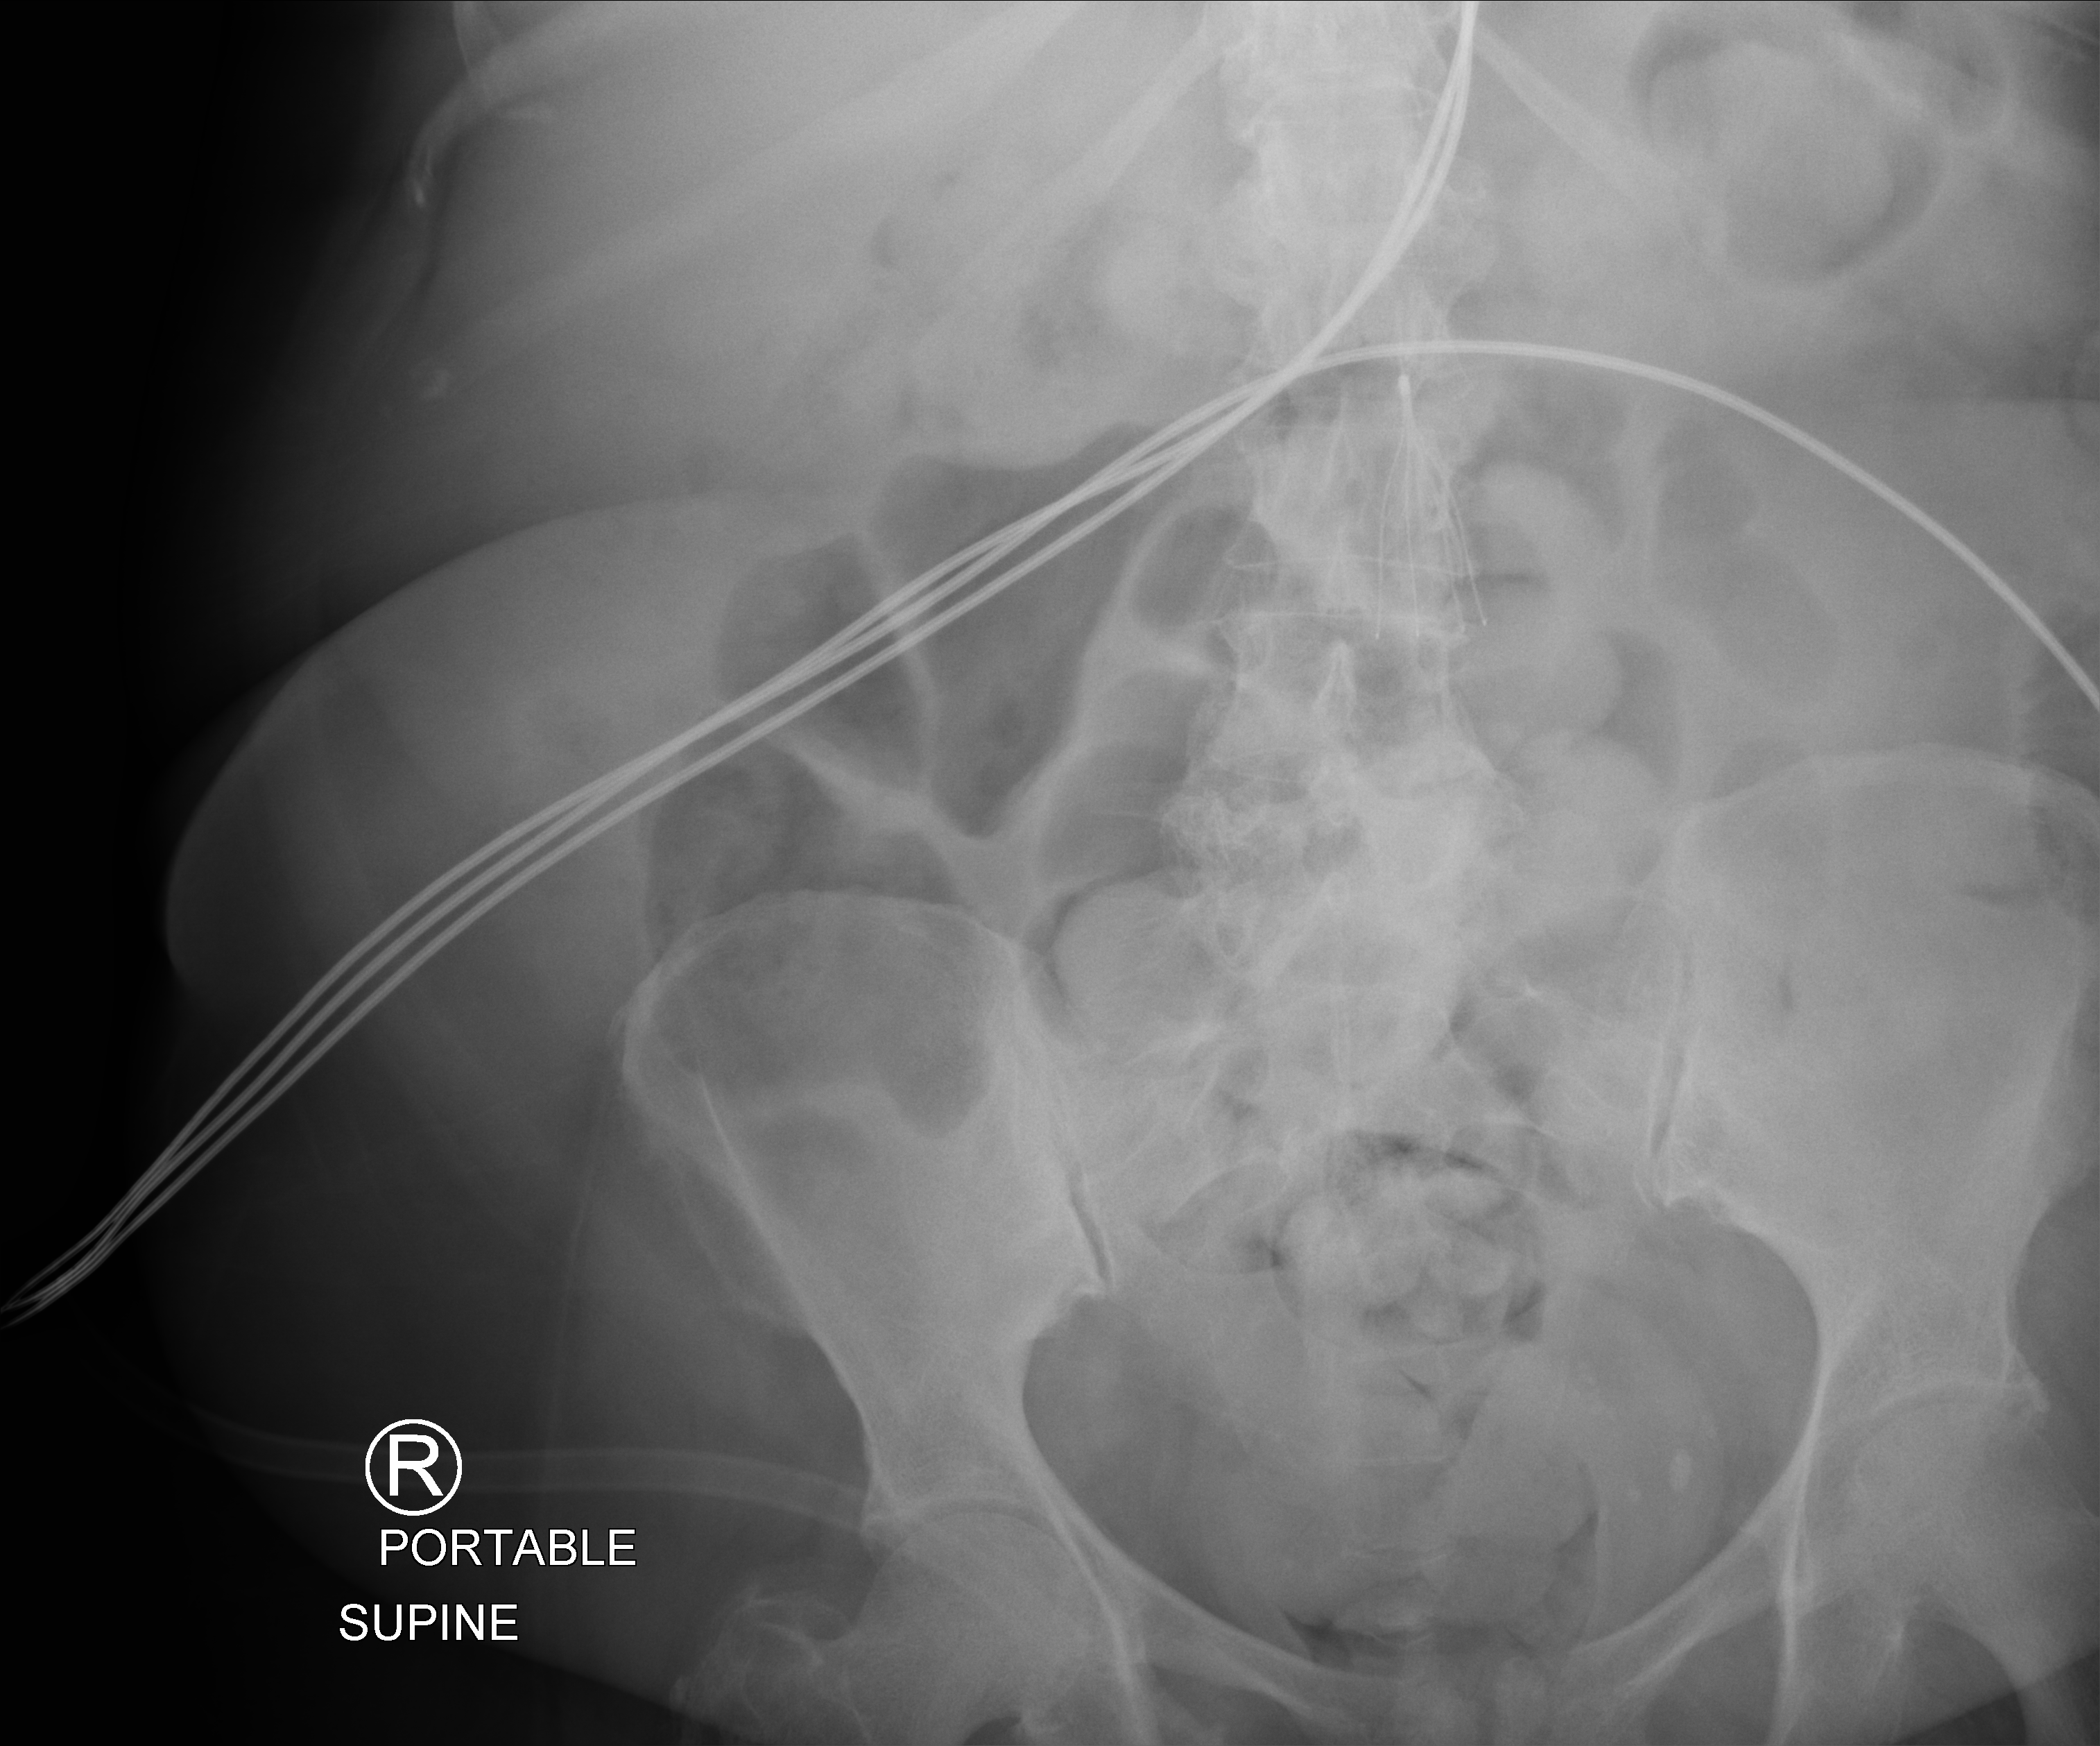
Bedside abdomen radiograph (computed radiography). Female patient hospitalised with COVID-19, age 60–74 years.
From the hospital-stay record, not from the radiograph (when in the stay this image was taken is not recorded):
- admitted to intensive care during this hospital stay: no